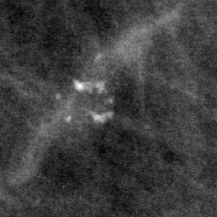
Crop from a digitized film mammogram around one marked abnormality, left breast, MLO view, BI-RADS breast density category 2 (scale 1–4).
Calcifications, morphology pleomorphic, distribution clustered; BI-RADS assessment category 4; subtlety rating 3 on a 1 (subtle) to 5 (obvious) scale; pathology result (as recorded, not read from the image): benign.